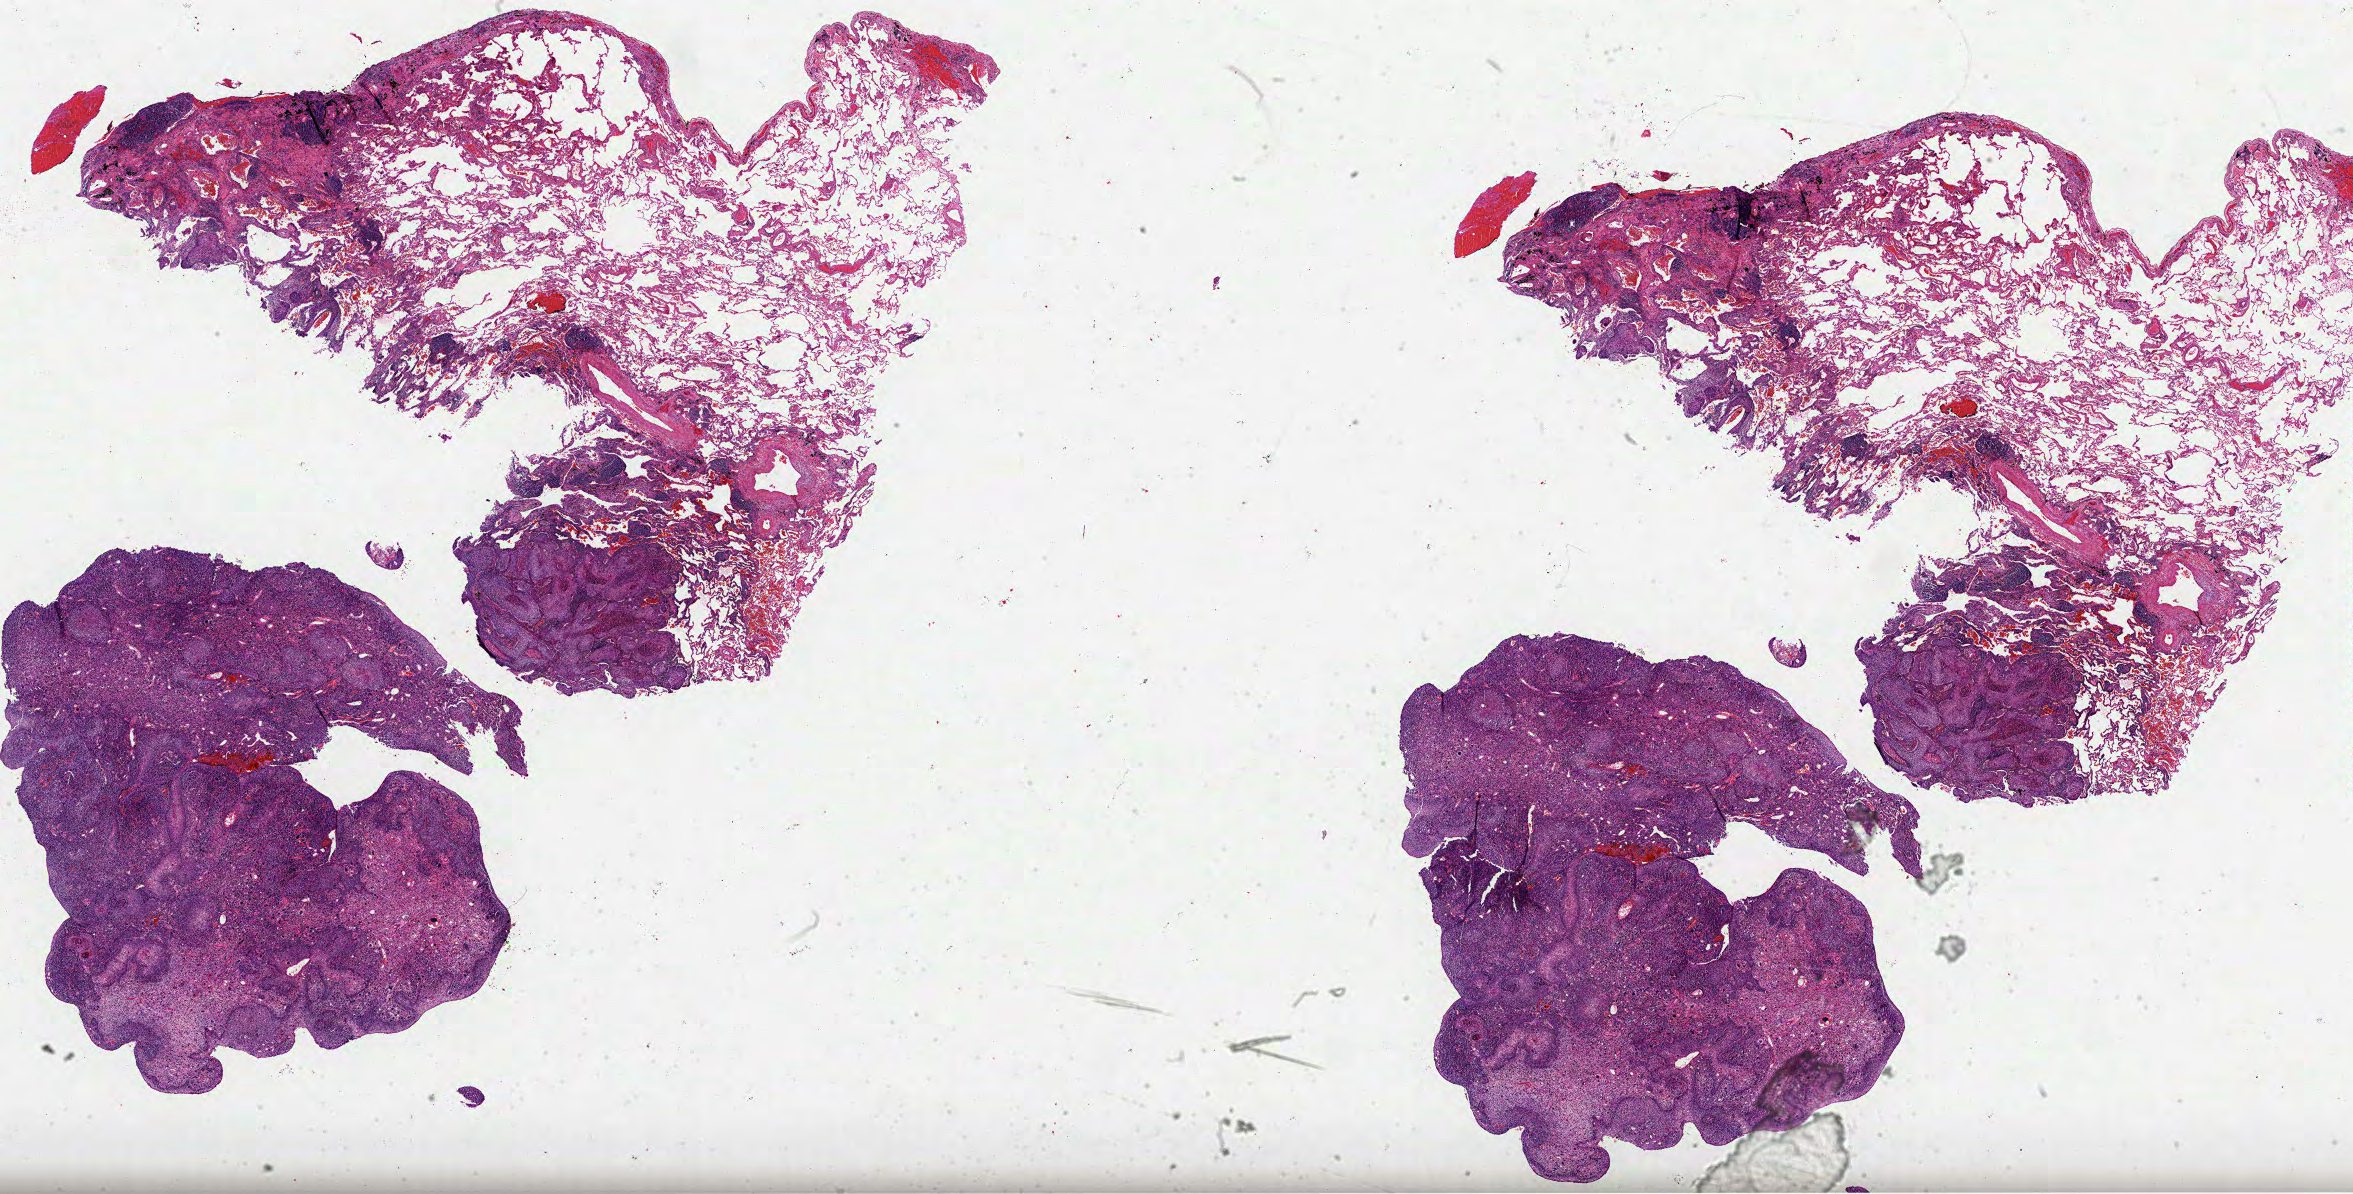
Whole-slide histology image, H&E, whole scanned area (about 38.0 x 19.3 mm, acquisition: 40x scan) shown as a low-resolution overview; FFPE section; sample: primary tumour, lung. Patient: female, age at initial diagnosis 76 years.
- AJCC pathologic stage: IB (5th edition)
- laterality: left
- diagnosis: Squamous cell carcinoma, NOS